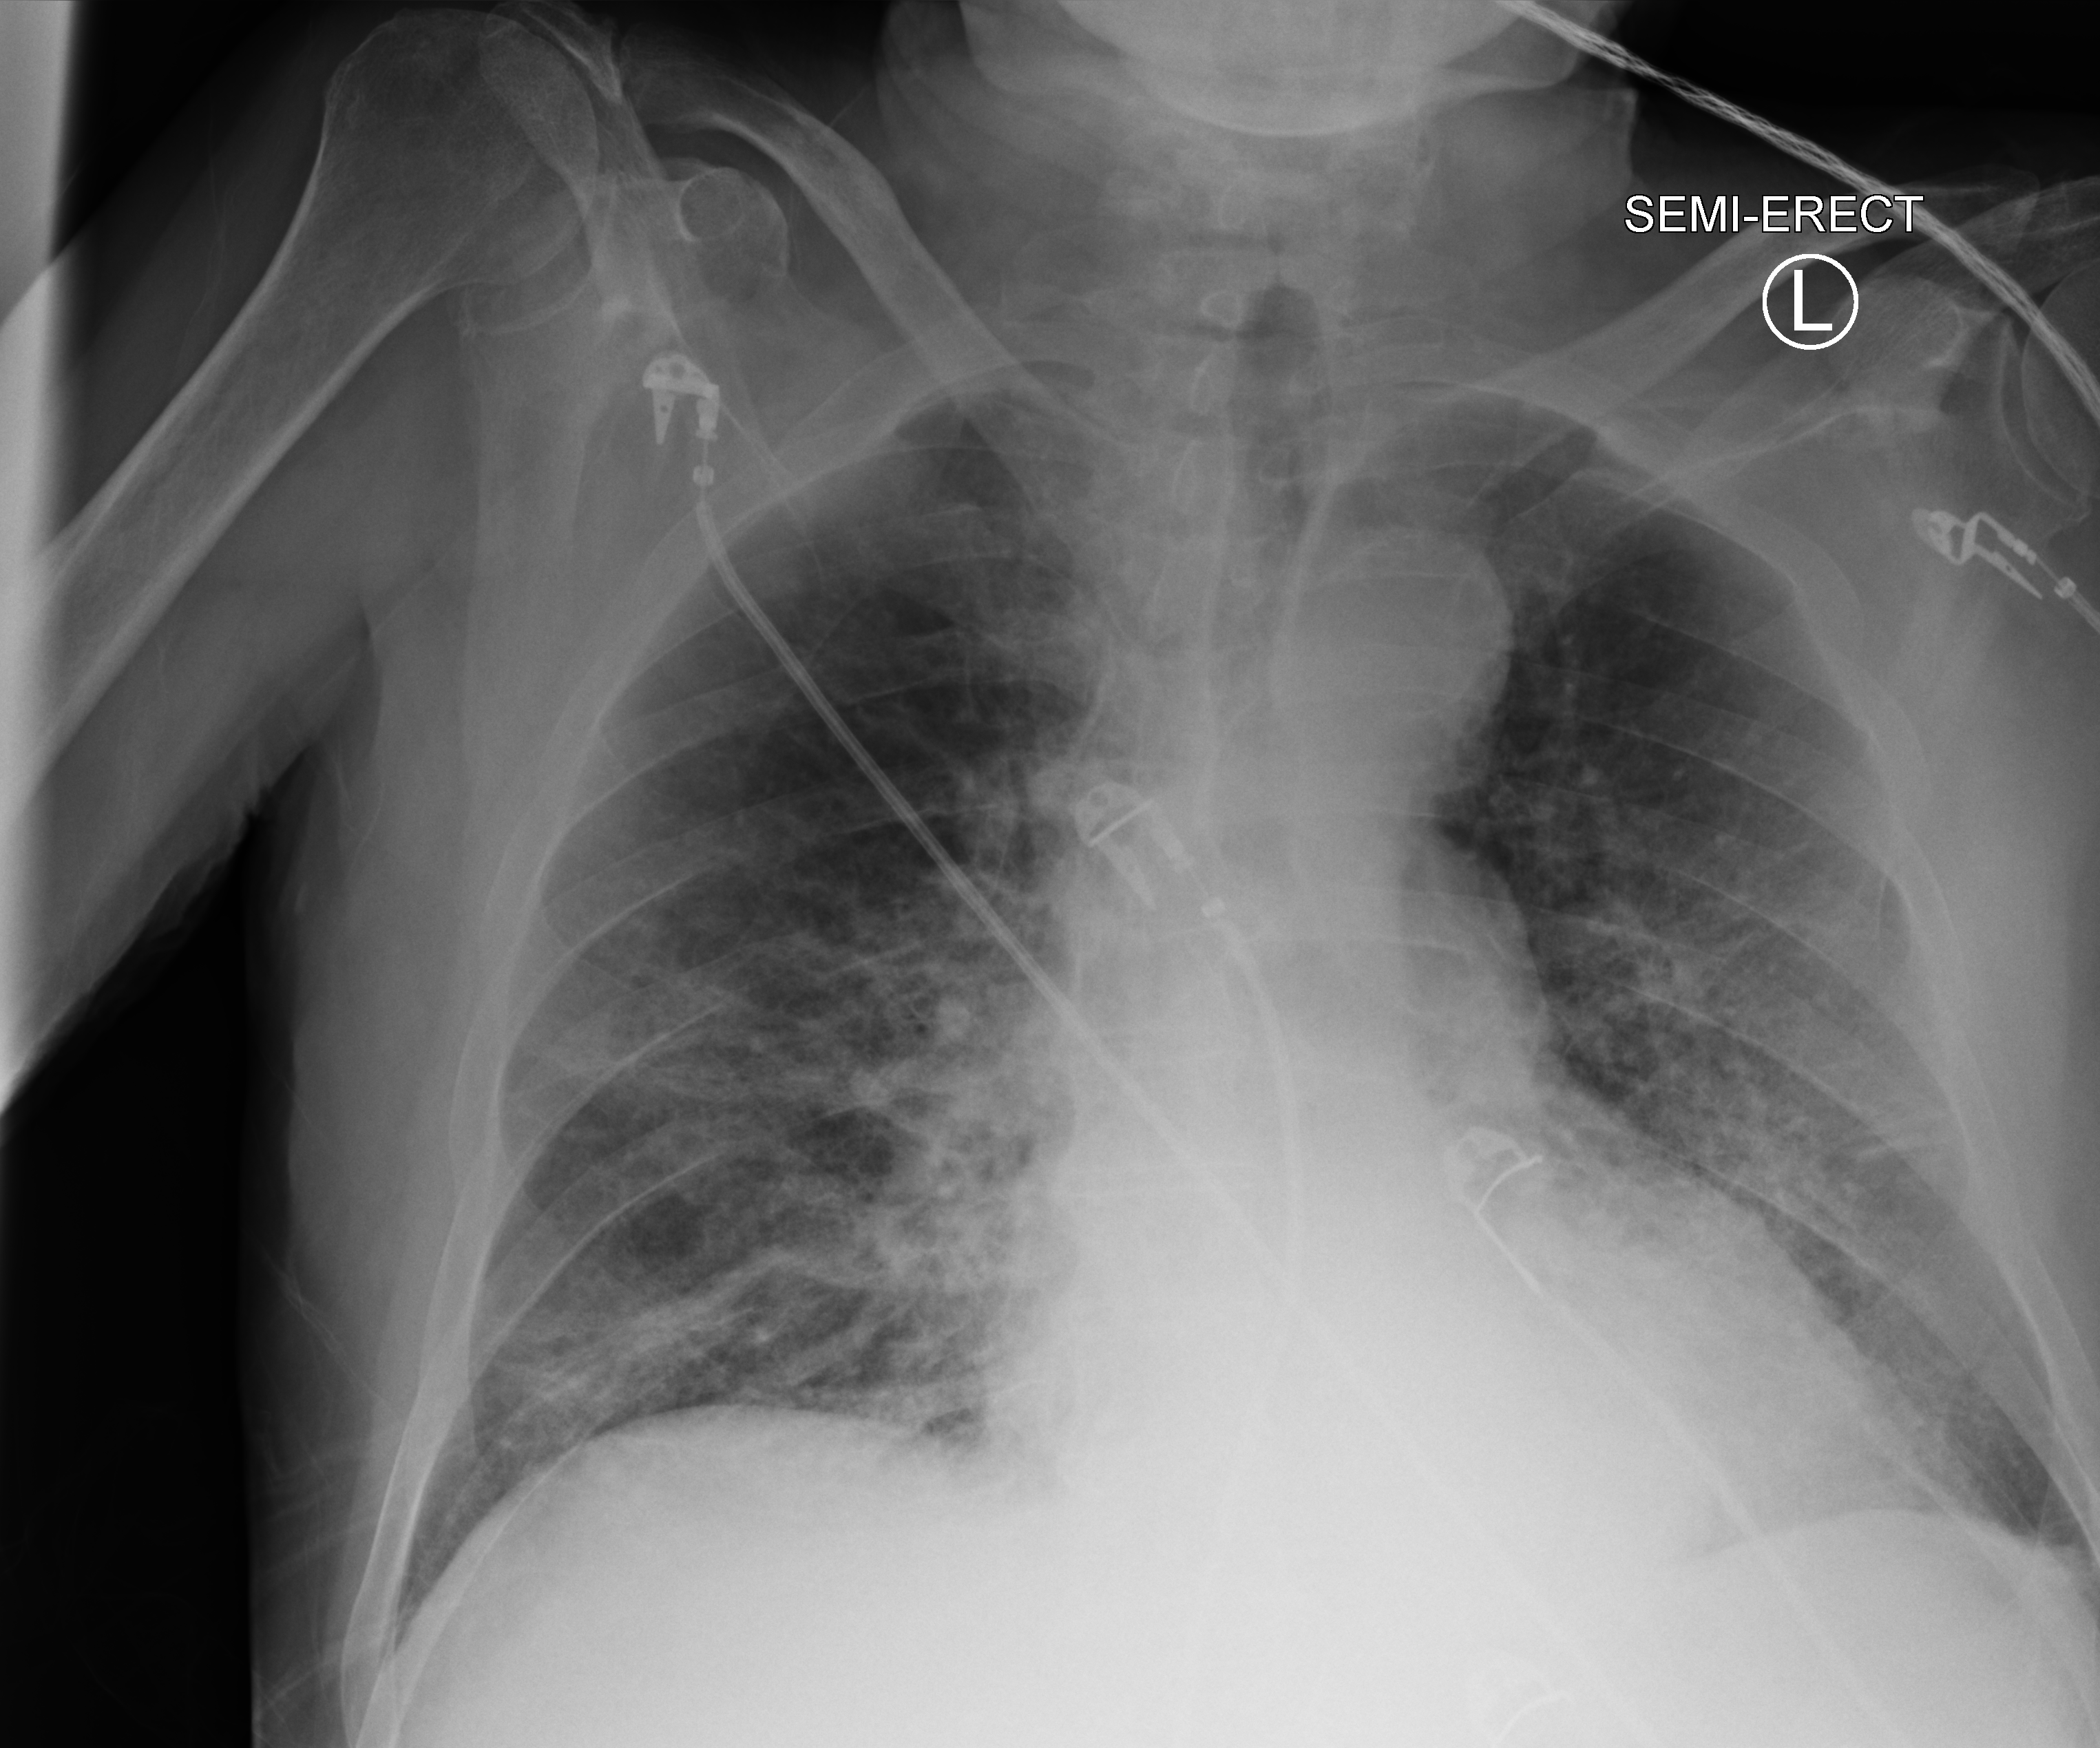
Bedside chest radiograph (computed radiography). Male patient hospitalised with COVID-19, age 75–90 years.
Admission-level facts for this patient (not findings on this image; timing relative to this image not recorded):
- admitted to intensive care during this hospital stay: yes
- length of hospital stay: 10 days
- COPD (admission record): no